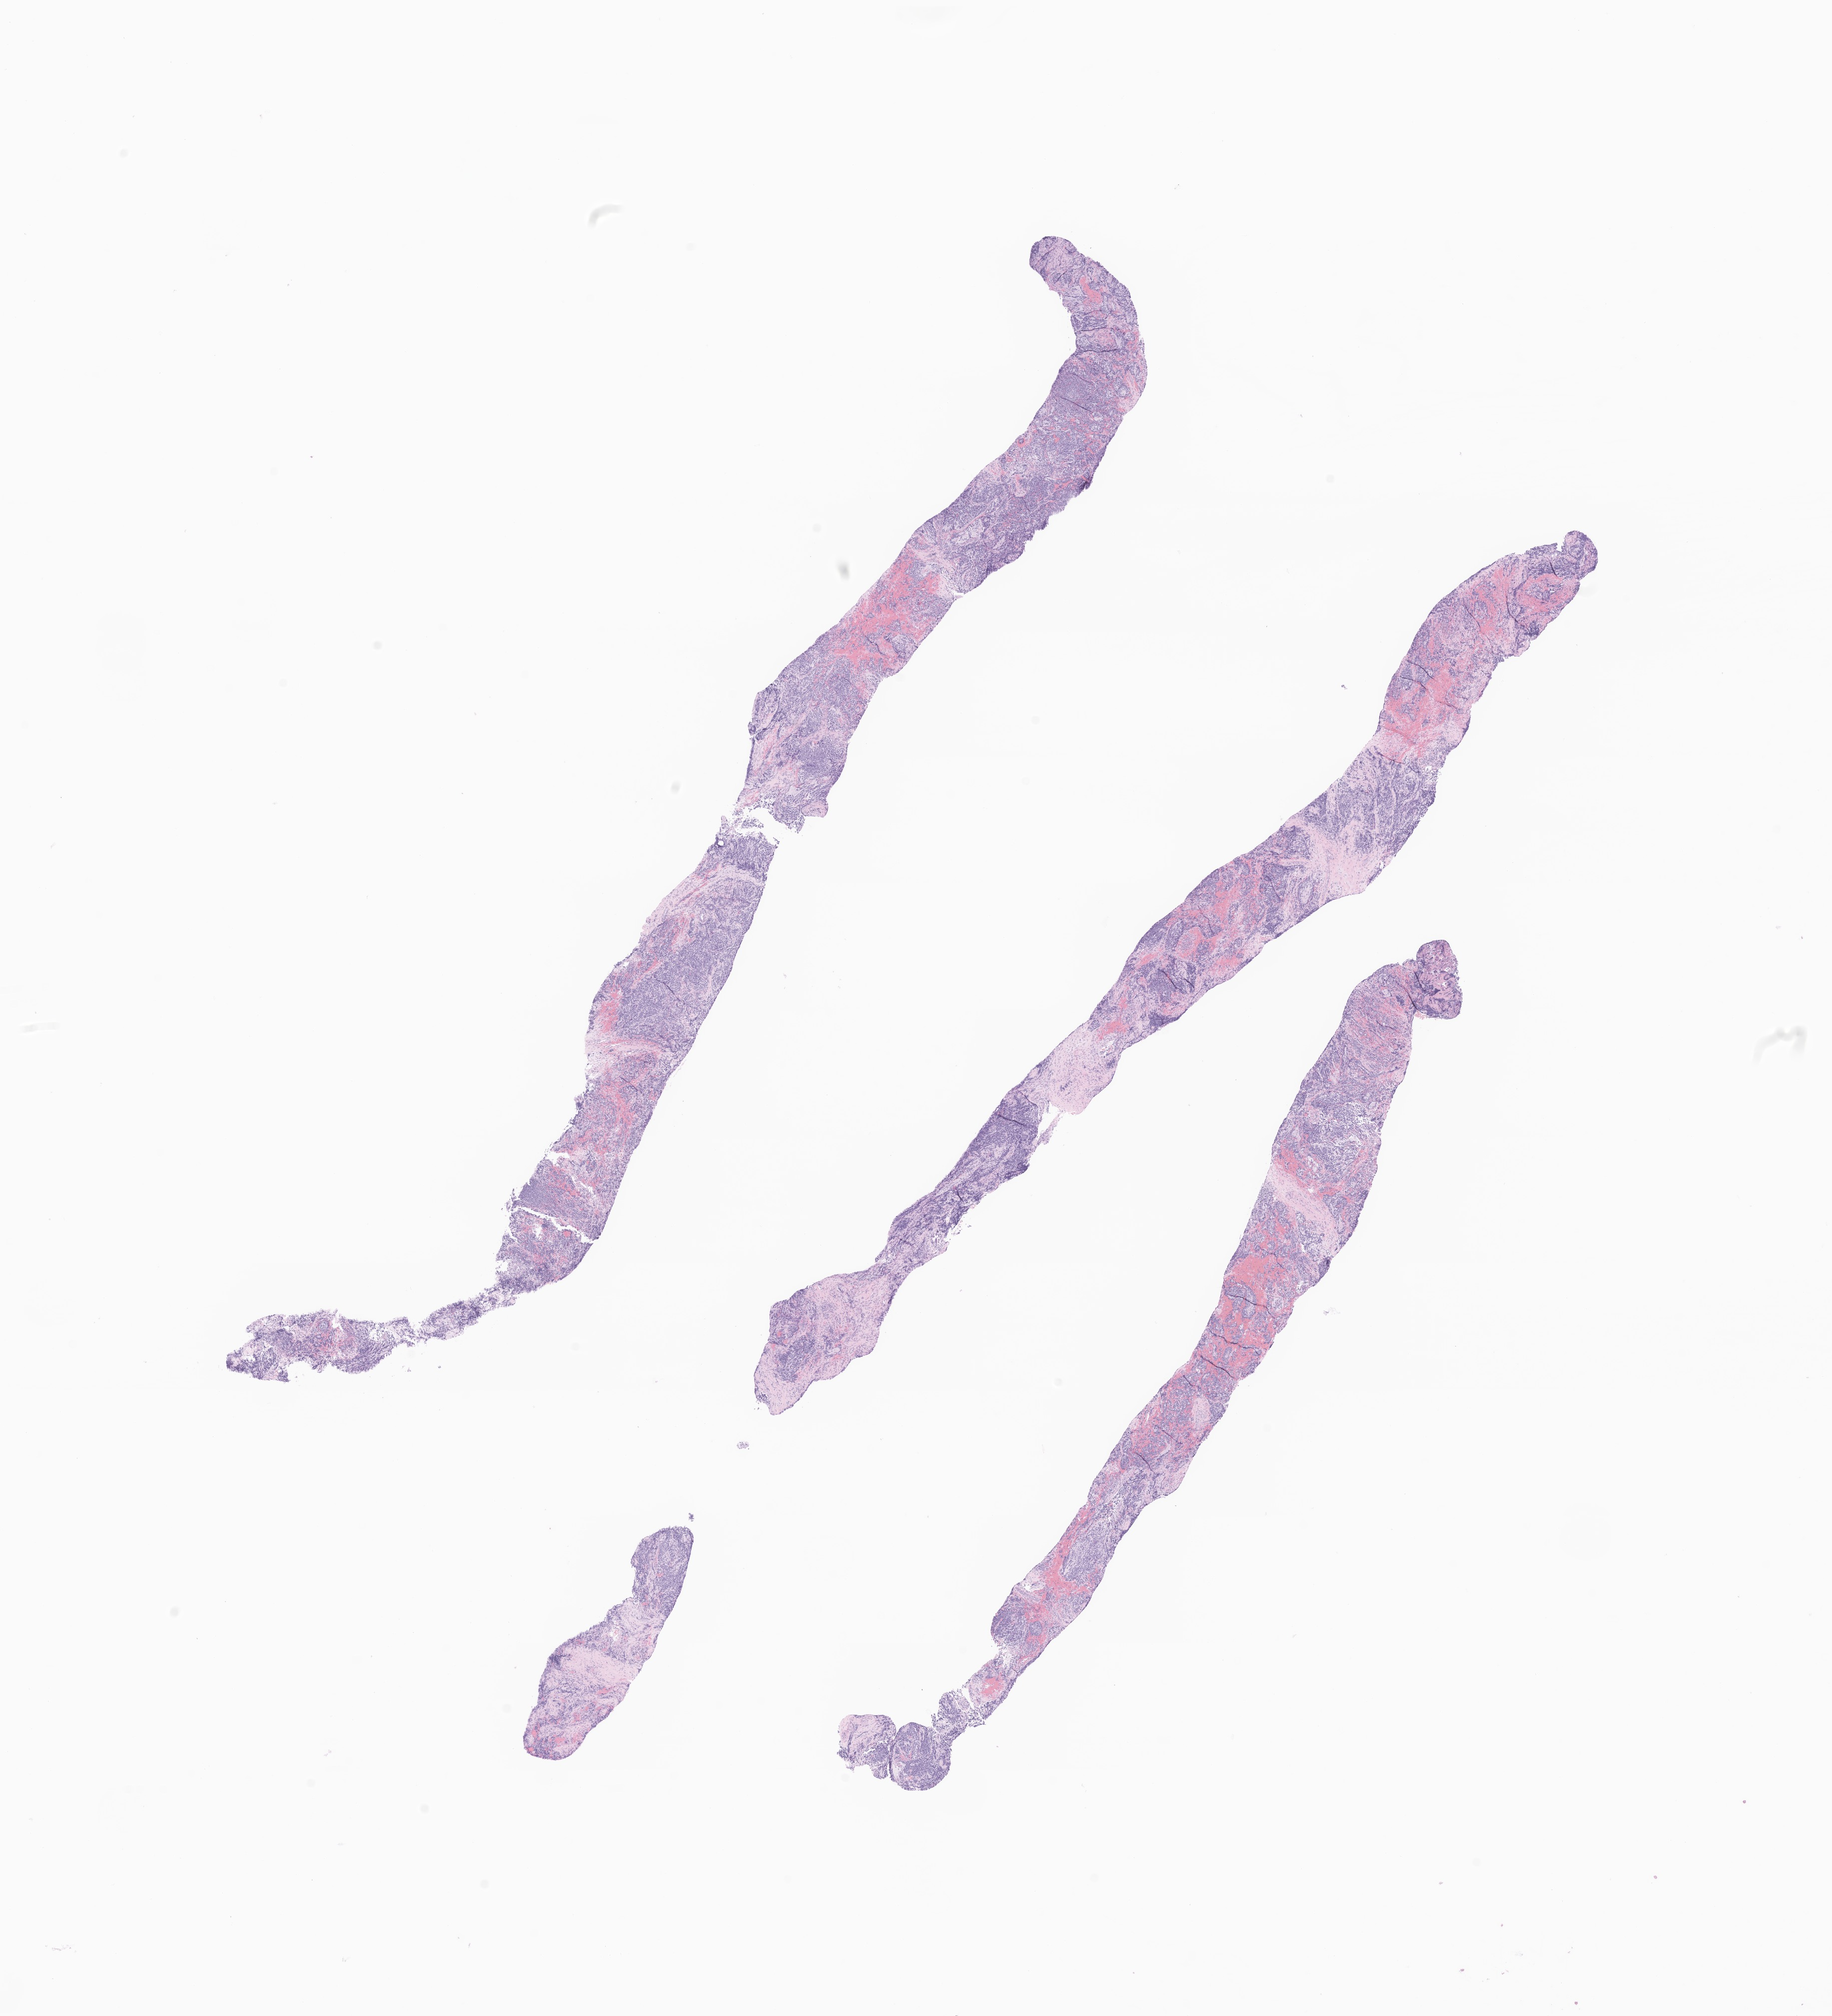
Hematoxylin and eosin (H&E) whole-slide image of tumor tissue from the adrenal gland — shown as a low-resolution overview of the whole scanned area (about 15.5 x 17.0 mm); FFPE section. Patient: male, age 871 days.
Diagnosis: Neuroblastoma, NOS.